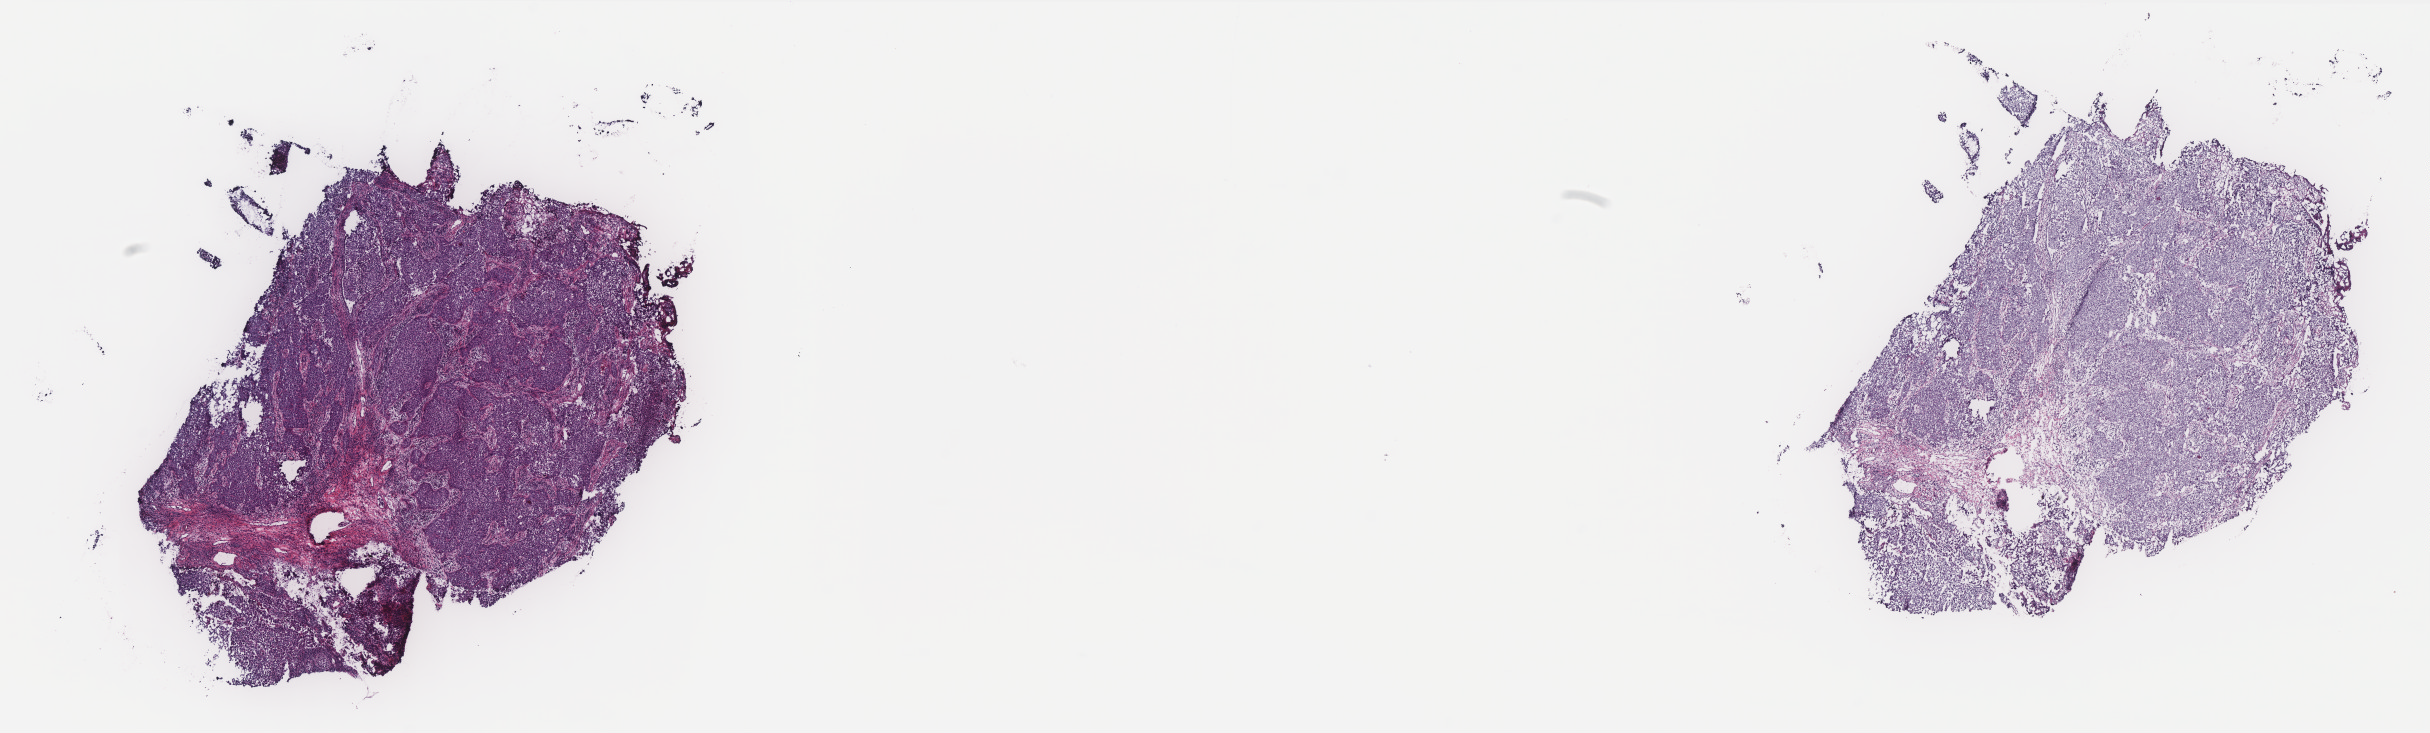
Whole-slide histology image, Hematoxylin and eosin (H&E) stained — low-resolution overview of the scanned area, about 19.5 x 5.9 mm (slide scanned at 40x). Frozen section. Cervix, primary tumour sample. Female, age 50 years at initial diagnosis. Pathologist review of this section (percent, as recorded): tumour cells 80%, tumour nuclei 80%.
Diagnosis: Squamous cell carcinoma, NOS (cervix uteri).